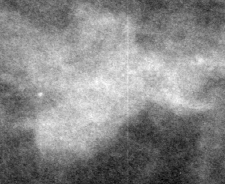
Crop from a digitized film mammogram around one marked abnormality; left breast; CC view.
Finding: mass, shape oval, margins microlobulated; BI-RADS assessment category 4; pathology result (as recorded, not read from the image): malignant.